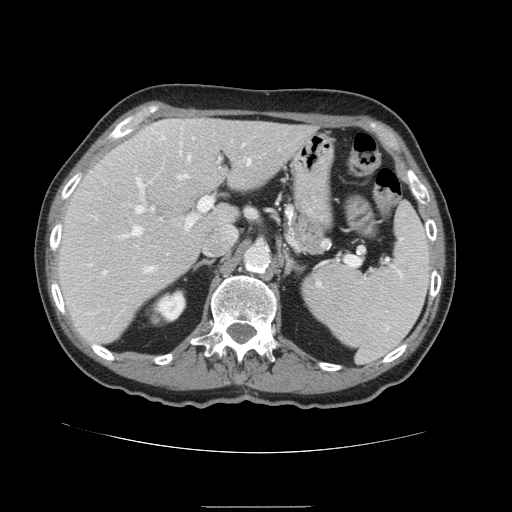
Contrast-enhanced abdominal CT, one axial slice. Position 97 of 168 along the scan axis. 120 kVp. Intravenous contrast given. Soft-tissue window (W 400 / L 40 HU). 512 × 512 image matrix, field of view 386 × 386 mm. Male patient, age 74 years. From the clinical record (not read from this slice): diagnosis: colorectal cancer liver metastases, imaged before liver resection; multiple liver metastases: no; largest metastasis: 14.5 cm; chemotherapy before resection: no.
Annotated regions visible in this slice (outlined manually by an expert reader):
- hepatic veins: bounding box (x1, y1, x2, y2) in pixels: (122, 157, 251, 270)
- liver: (58, 119, 317, 345)
- planned liver remnant (the part of the liver to remain after resection): (58, 119, 317, 345)
- portal vein (with intrahepatic branches): (93, 179, 212, 273)